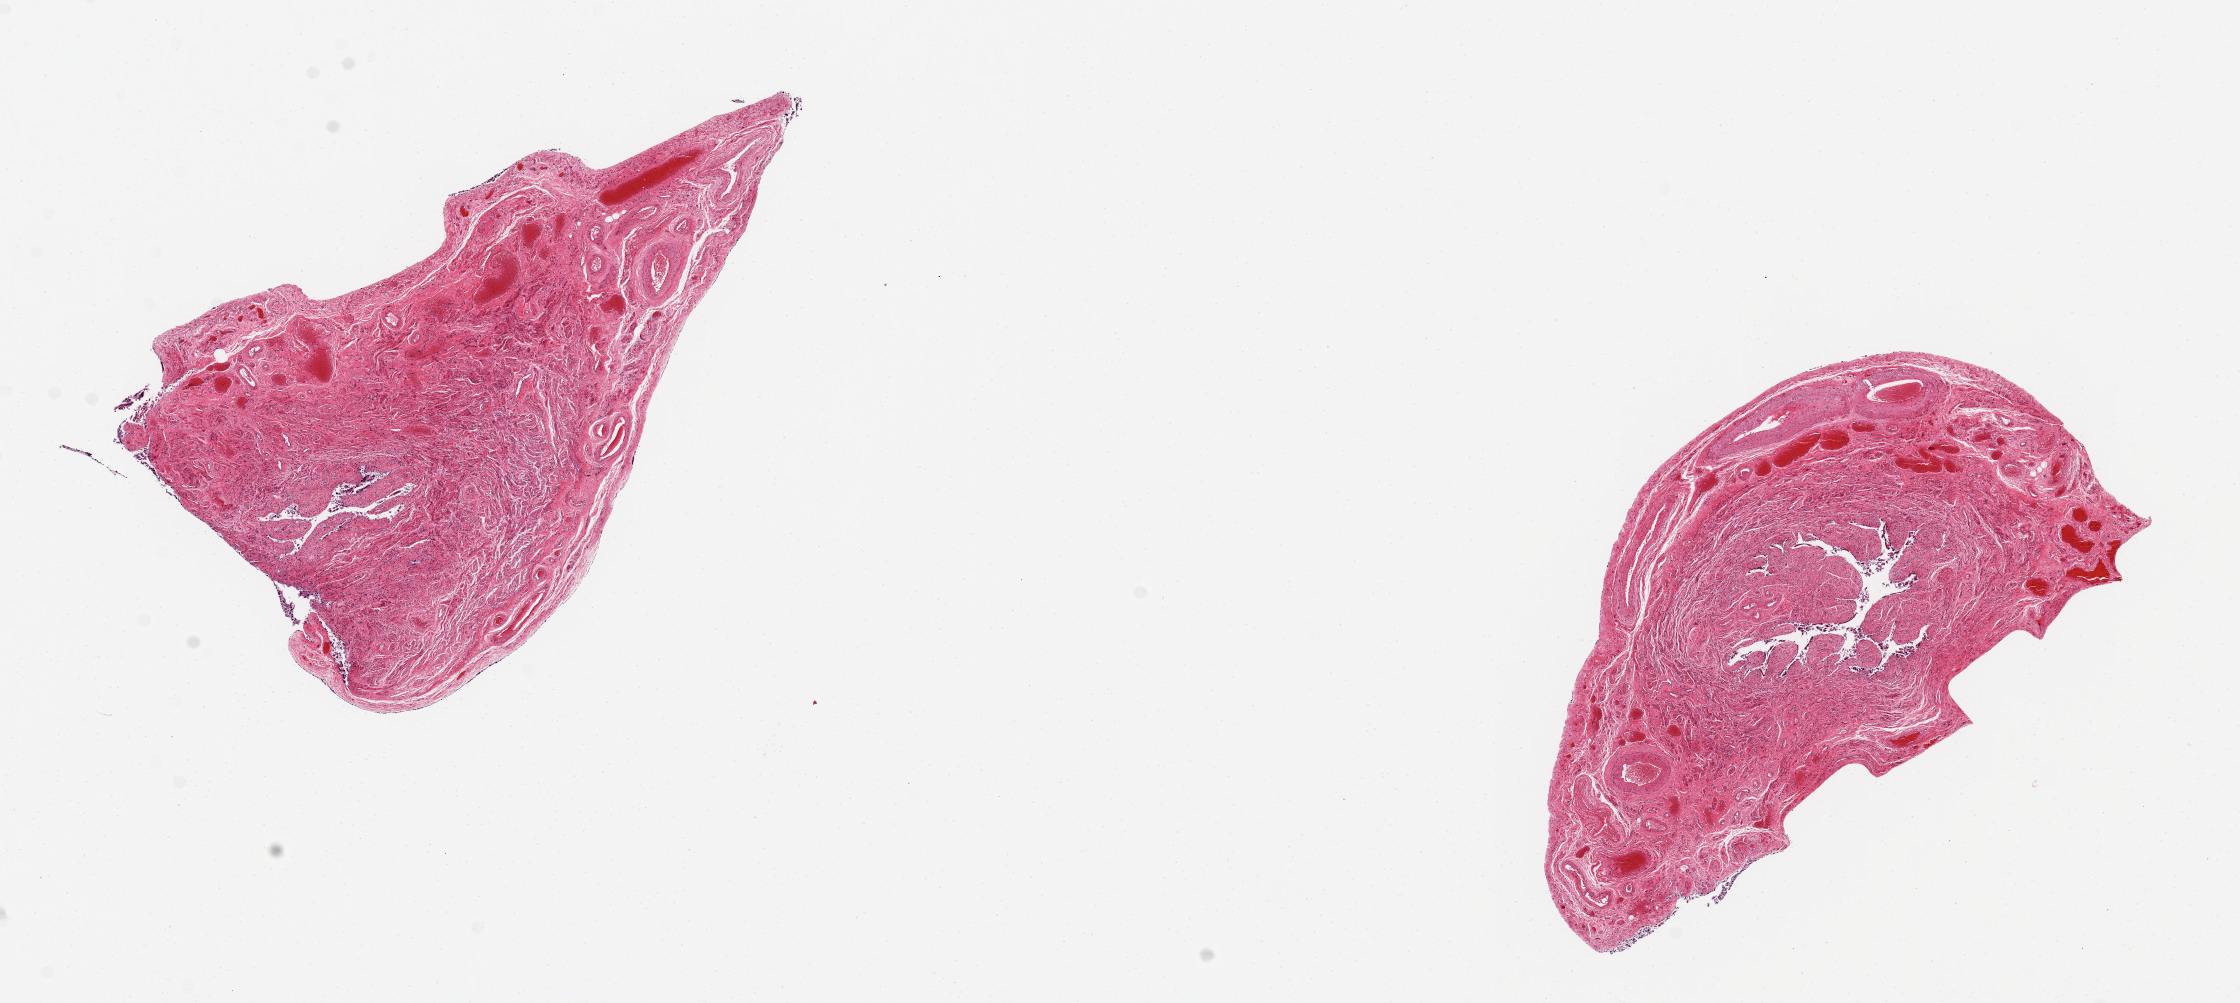
Whole-slide image, hematoxylin and eosin (H&E) stain, shown as a low-resolution overview of the whole scanned area (about 17.7 x 7.9 mm); PAXgene-fixed paraffin-embedded (PFPE) section; sampled site (target tissue): fallopian tube; tissue donor sample. Donor: female.
Reviewer comment on this tissue sample: 2 ~5x4mm aliquots, luminal mucosa totally autolyzed.